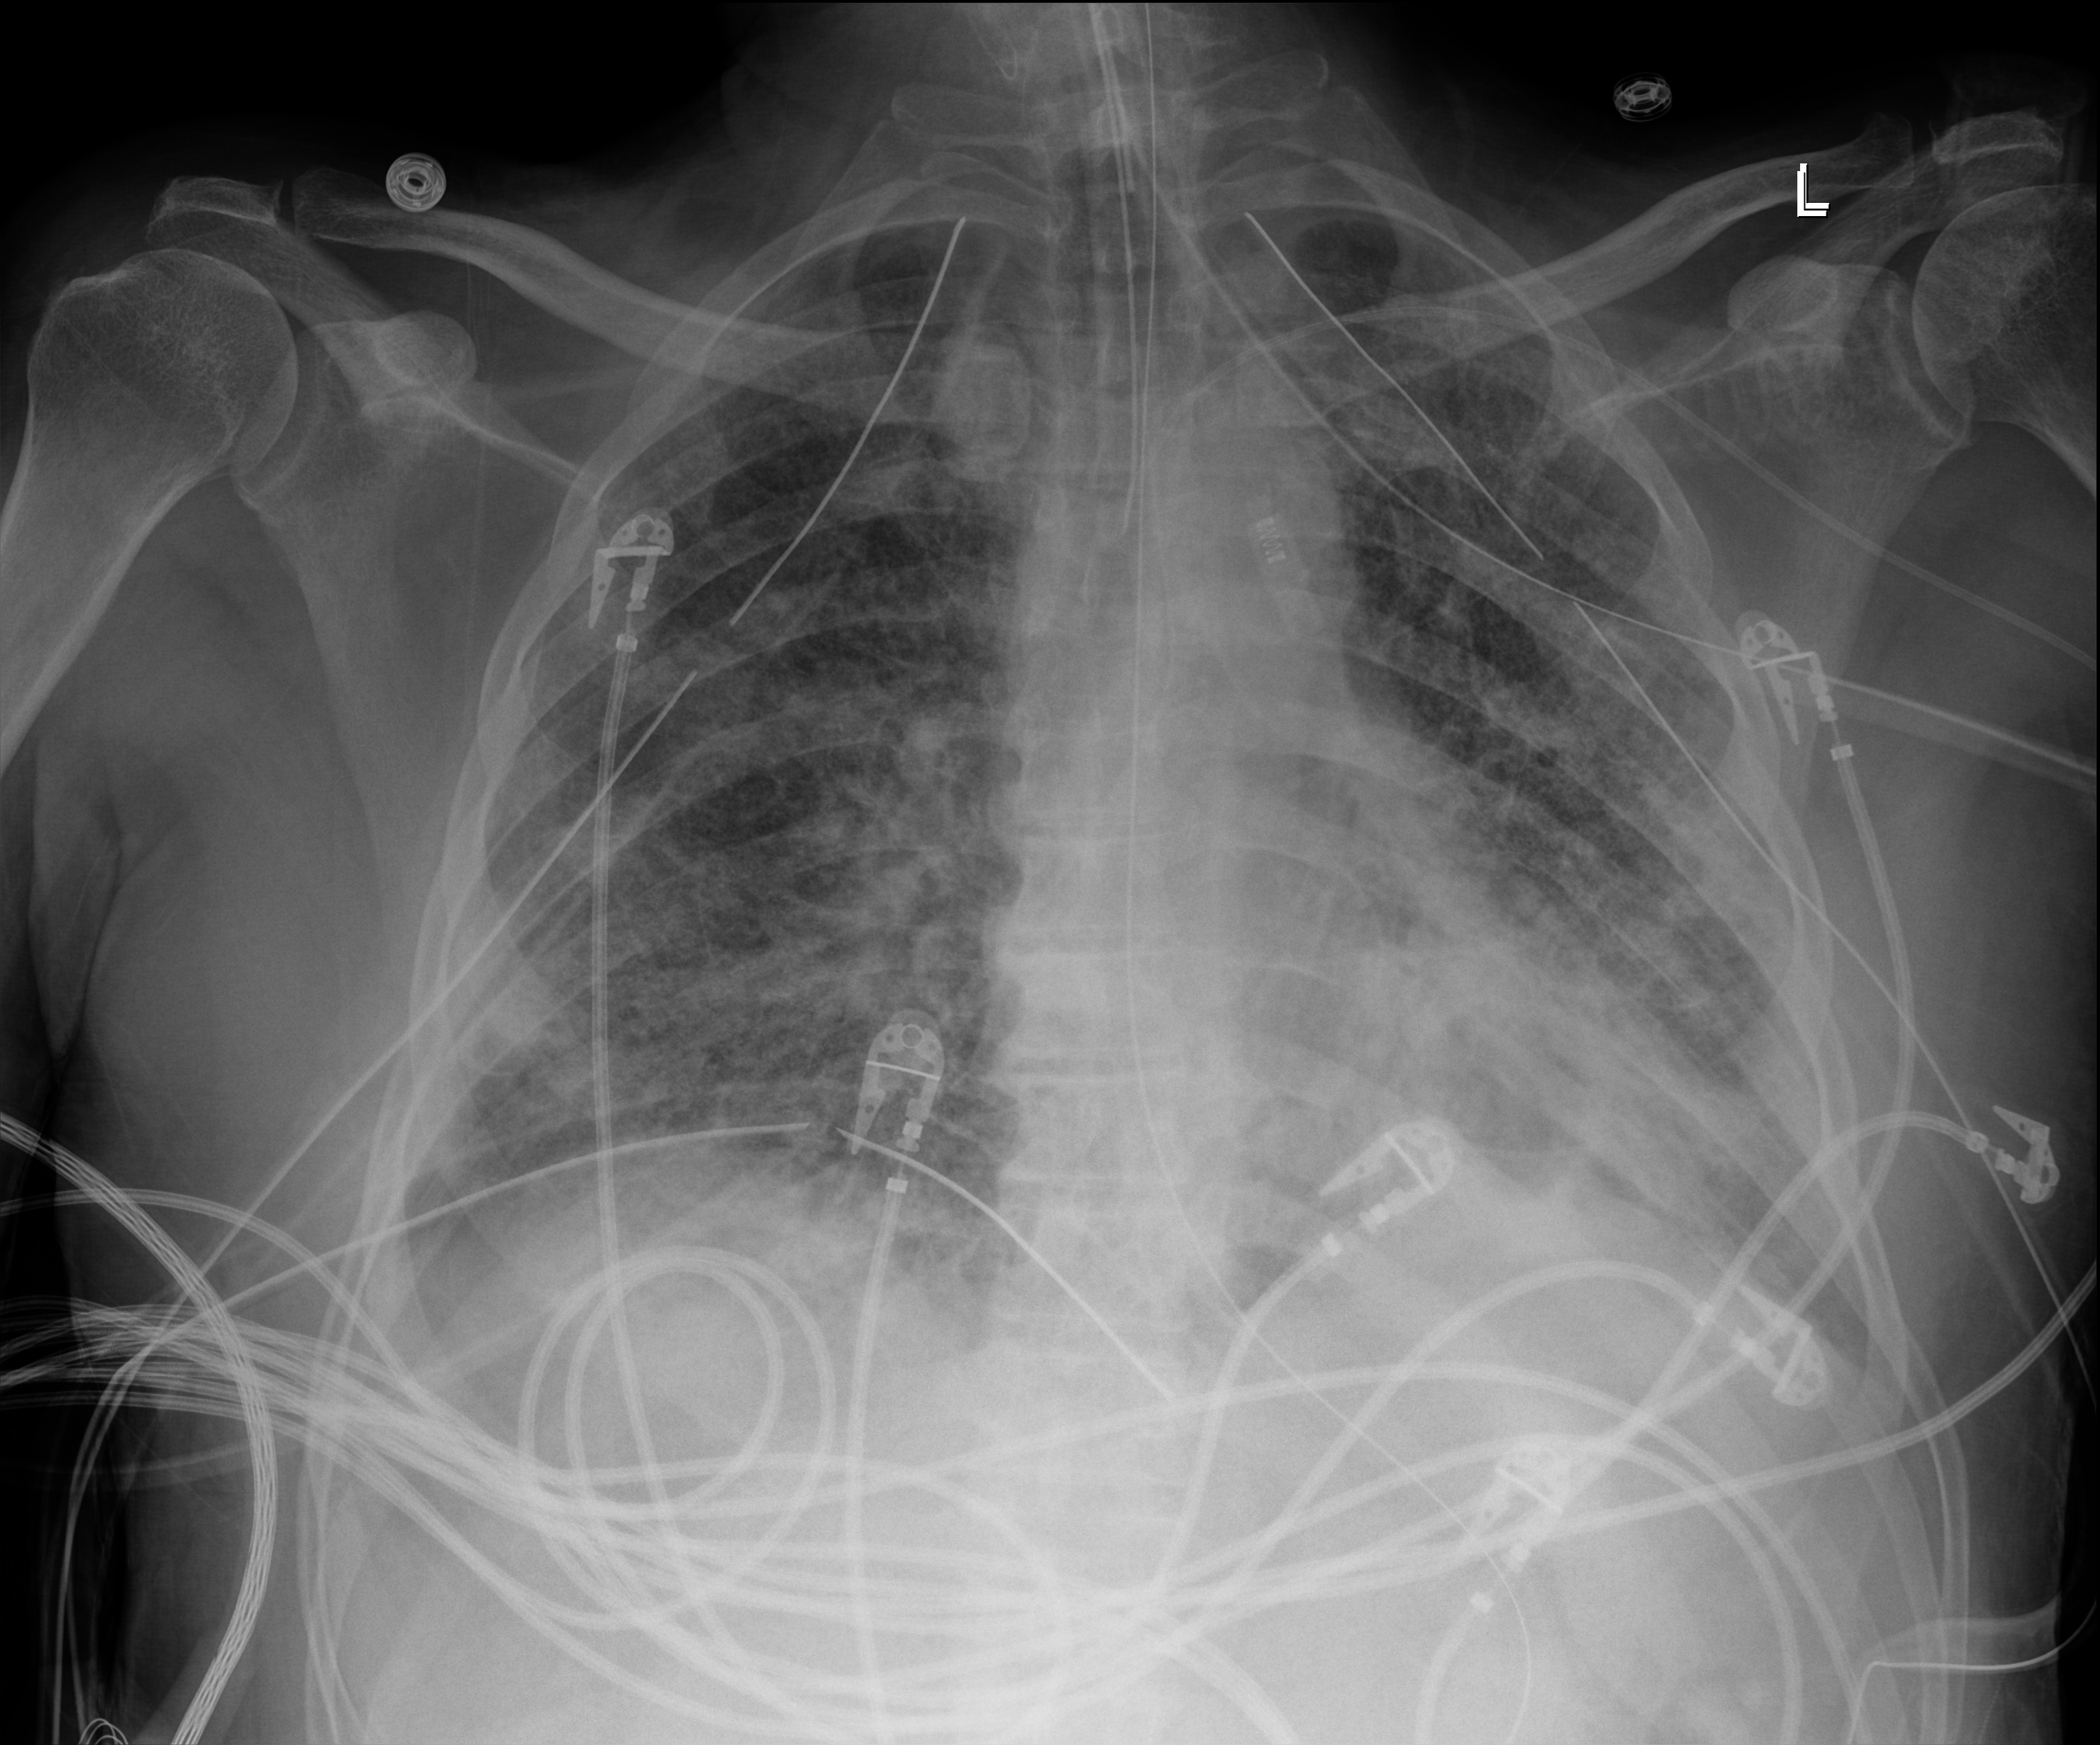
Bedside chest radiograph (digital radiography), anteroposterior (AP) projection. Male patient hospitalised with COVID-19, age 18–59 years.
Hospital-stay facts (about this admission, not read from this image; timing relative to this image not recorded): admitted to intensive care during this hospital stay: yes; mechanically ventilated during this hospital stay: yes; diabetes (admission record): no.